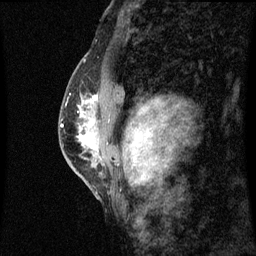
Breast MRI (dynamic contrast-enhanced), one sagittal slice; slice 38 of 60 in the series (ordered by position); dynamic contrast-enhanced series, image 2 of 3 at this slice position (ordered by acquisition); 1.5 T; TE 4.2 ms, TR 8.9 ms; 2 mm slice thickness; 256 × 256 image matrix, field of view 200 × 200 mm. Patient: female, 50 years. From the clinical record (not read from this slice): setting: breast cancer imaged before/during neoadjuvant chemotherapy; receptor status: triple-negative.
Outlined on this slice (semi-automatically segmented with operator editing):
- analysis volume of interest (the breast-tissue region the enhancement analysis was run in; not a lesion): bounding box (x1, y1, x2, y2) in pixels: (68, 80, 100, 169)
- tumour enhancement mask (voxels above the 70 % enhancement threshold inside the analysis volume of interest): (80, 96, 98, 149)